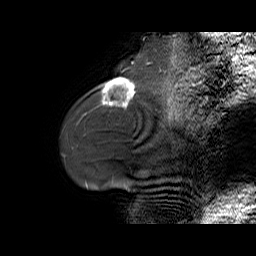
Breast MRI (dynamic contrast-enhanced), one sagittal slice; dynamic contrast-enhanced series, time point 2 of 6 at this slice position (early post-contrast); 1.5 T; TE 5.5 ms, TR 32.9 ms; 4 mm slice thickness; 256 × 256 image matrix, field of view 240 × 240 mm. Female patient. Case-level facts recorded for this patient, not image findings: setting: breast cancer imaged before/during neoadjuvant chemotherapy; receptor status: HER2-positive.
Outlined on this slice (semi-automatically segmented with operator editing):
- analysis volume of interest (the breast-tissue region the enhancement analysis was run in; not a lesion): box from (x=96, y=78) to (x=141, y=107) px
- tumour enhancement mask (voxels above the 100 % enhancement threshold inside the analysis volume of interest): (x=102, y=78)–(x=135, y=107)